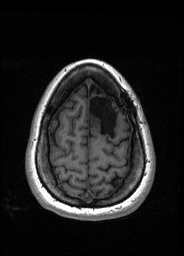
Pre-operative brain MRI before brain-tumour surgery, one axial slice. Slice 41 of 176 in the series (ordered by position). T1-weighted post-contrast. 184 × 256 image matrix, field of view 180 × 250 mm. Case-level facts recorded for this patient, not image findings: histopathology: Oligodendroglioma; WHO grade: 2; IDH mutation: yes; tumour location: Left Frontal.
Structures marked on this image (outlined manually by an expert reader):
- tumour: bounding box (x1, y1, x2, y2) in pixels: (89, 114, 101, 127)